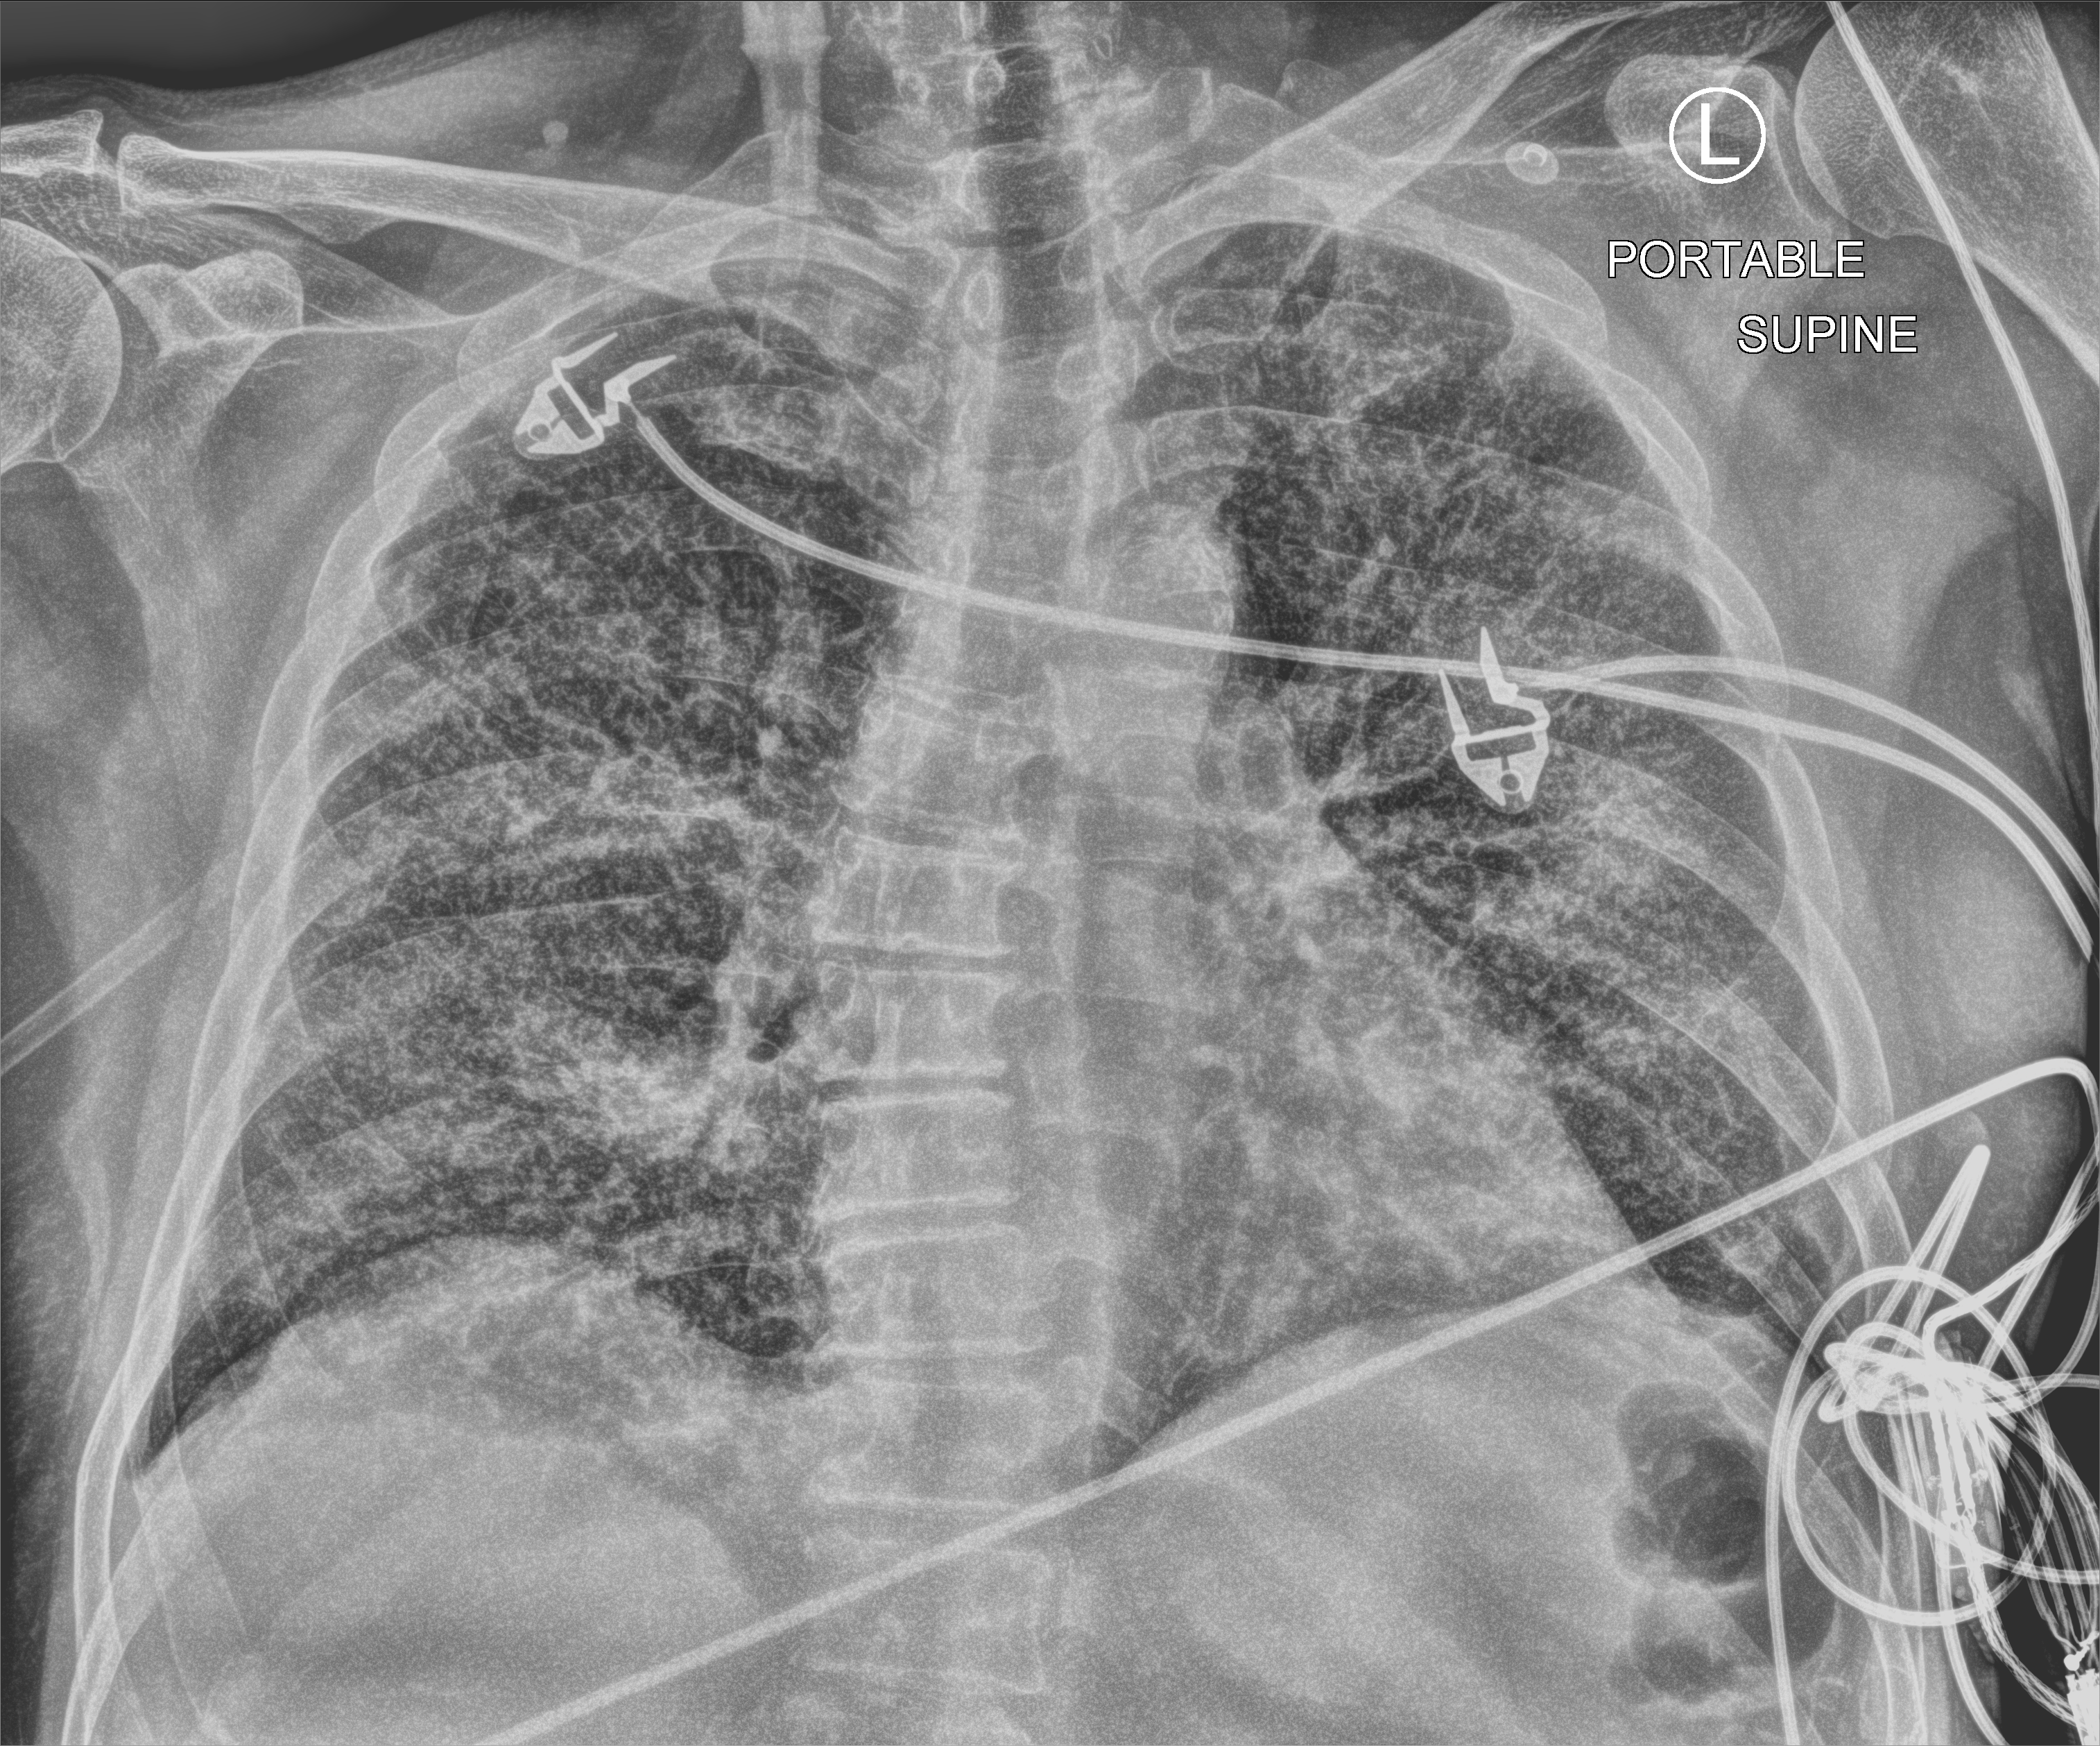
Portable chest radiograph; anteroposterior (AP) projection. Male patient hospitalised with COVID-19, age 18–59 years.
From the hospital-stay record, not from the radiograph (when in the stay this image was taken is not recorded):
- mechanically ventilated during this hospital stay: no
- admitted to intensive care during this hospital stay: no